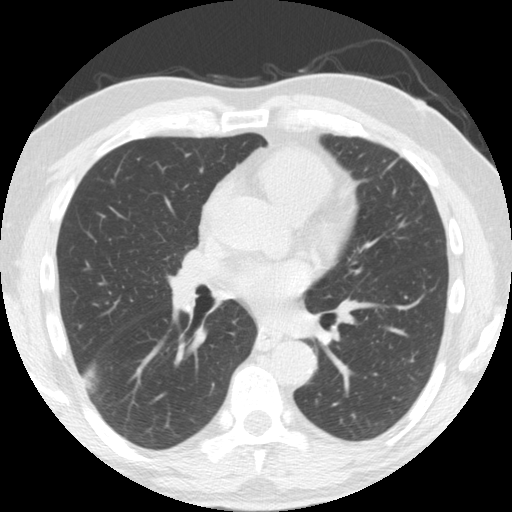
Axial slice from a low-dose chest CT screening exam; second annual screen; lung window (W 1500 / L -600 HU); standard (soft-tissue) reconstruction kernel (STANDARD). Male, age 61 years at enrolment.
Expert reader's lesion annotation, box from (x=54, y=329) to (x=123, y=404) px. Screening reader's record for this exam (one nodule recorded; not confirmed to be the boxed lesion): non-calcified nodule or mass ≥4 mm, right lower lobe, 33 × 19 mm, smooth margins, soft tissue attenuation, pre-existing on the prior screen: yes; interval growth: yes. Later outcome: lung cancer diagnosed 30 days after this screen — adenosquamous carcinoma, right lower lobe, poorly differentiated (G3), stage IV (AJCC 6th edition), 45 mm at pathology.